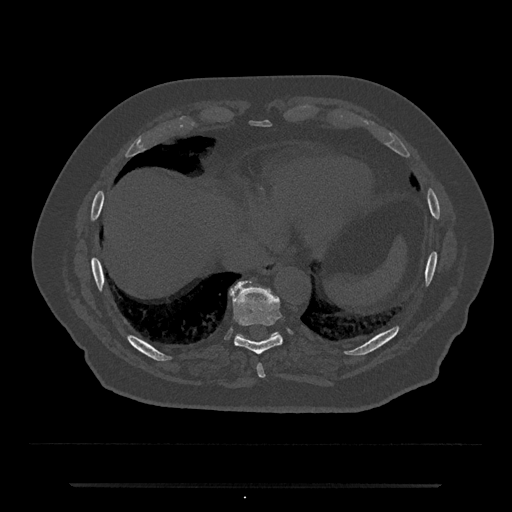
CT including the spine, one axial slice. Slice 749 of 797 in the series (ordered by position). Reconstruction kernel Br40s/3. 120 kVp. Bone window (W 1800 / L 400 HU). 0.5 mm slice thickness. 512 × 512 image matrix, field of view 434 × 434 mm. Patient: male, 80 years. From the clinical record (not read from this slice): primary cancer: prostate.
Annotated regions visible in this slice (semi-automatically segmented with operator editing):
- T10 vertebra: bounding box (x1, y1, x2, y2) in pixels: (230, 293, 280, 339)
- T8 vertebra: (257, 364, 265, 378)
- T9 vertebra: (230, 280, 282, 355)